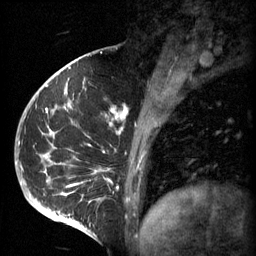
Breast MRI (dynamic contrast-enhanced), one sagittal slice; slice 23 of 60 in the series (ordered by position); 3 images stored at this slice position (order not interpretable as contrast timing); 1.5 T; TE 4.2 ms, TR 11 ms; 256 × 256 image matrix. Patient: female, 51 years.
Structures marked on this image (semi-automatically segmented with operator editing):
- analysis volume of interest (the breast-tissue region the enhancement analysis was run in; not a lesion): bounding box <48,82,161,197> (left, top, right, bottom; pixels)
- tumour enhancement mask (voxels above the 70 % enhancement threshold inside the analysis volume of interest): <48,82,146,195>